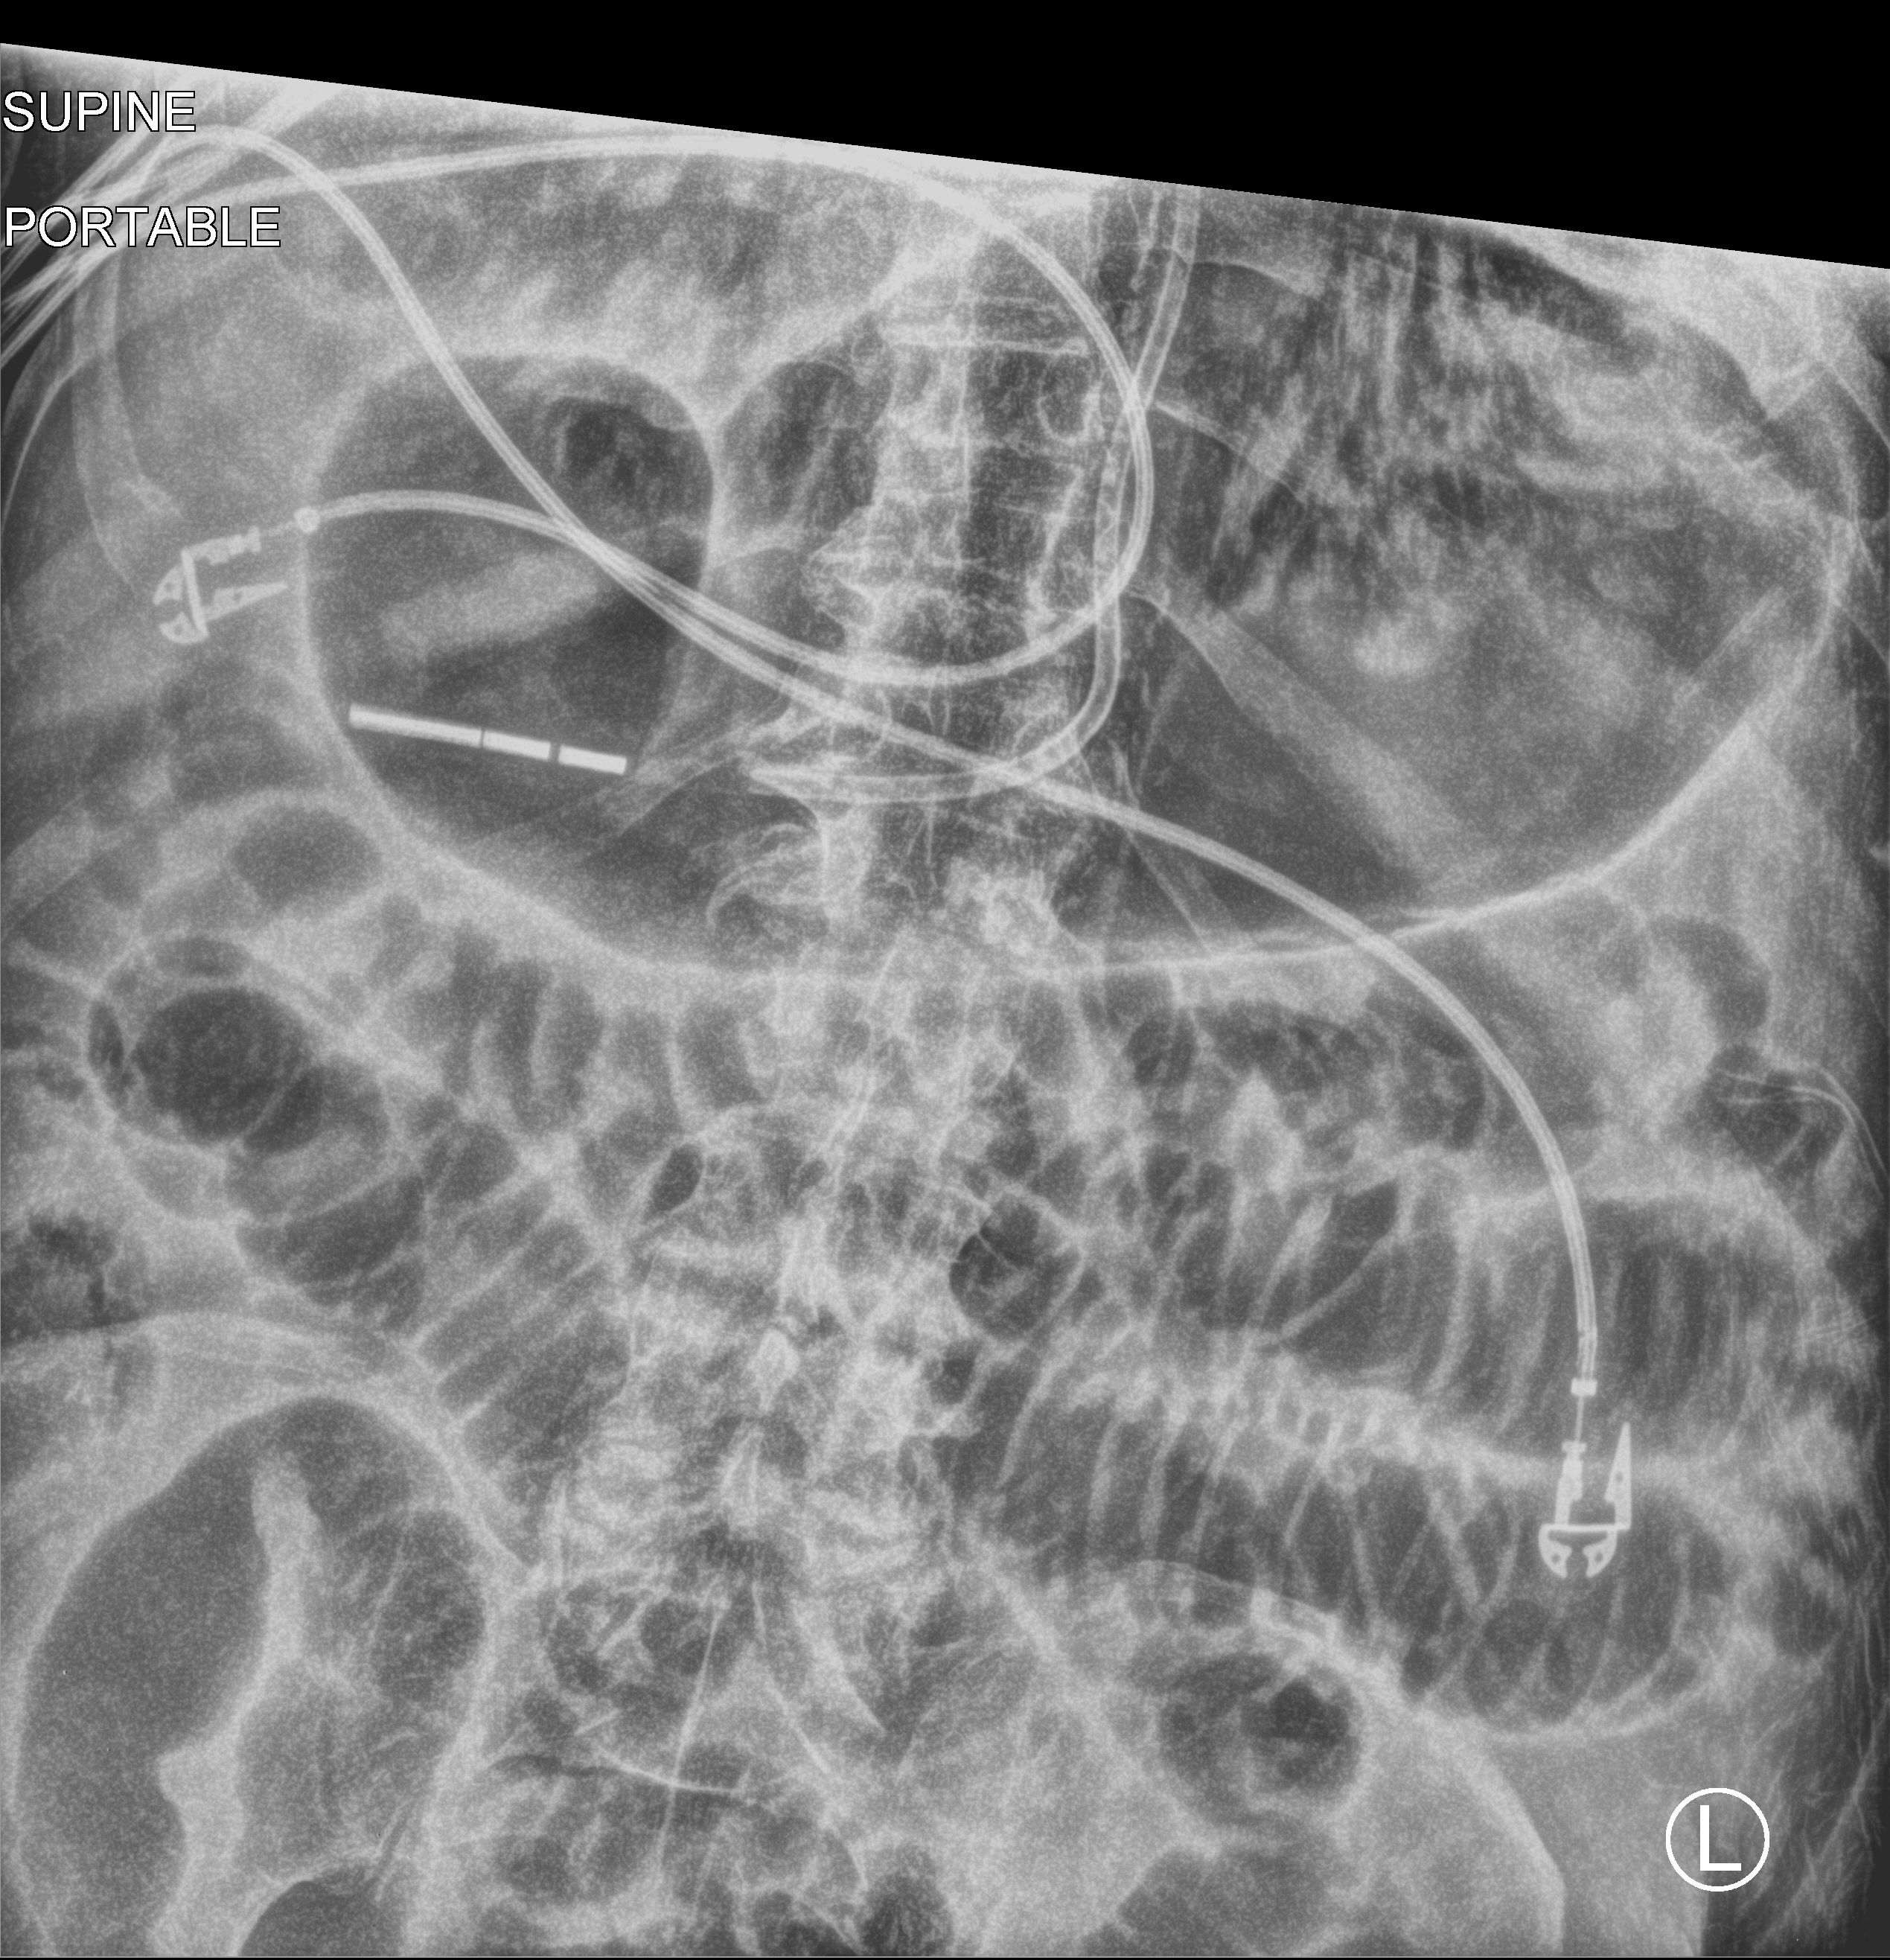
Bedside abdomen radiograph (computed radiography); anteroposterior (AP) projection. Patient hospitalised with COVID-19; male, aged 75–90 years.
From the hospital-stay record, not from the radiograph (when in the stay this image was taken is not recorded): length of hospital stay: 26 days; admitted to intensive care during this hospital stay: yes; hypertension (admission record): yes.